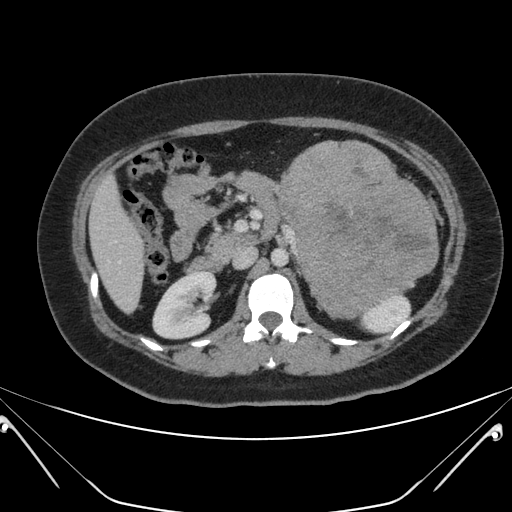
Contrast-enhanced abdominal CT, one axial slice. Slice 113 of 168 in the series (ordered by position). 120 kVp. Intravenous contrast given. Soft-tissue window (W 400 / L 40 HU). 3 mm slice thickness. 512 × 512 image matrix, field of view 394 × 394 mm. Patient: female, 26 years. From the clinical record (not read from this slice): diagnosis: adrenocortical carcinoma; tumour side: left adrenal; tumour size at pathology: 28 cm; Ki-67 index: 20 %; stage (as recorded): 2.
Structures marked on this image (semi-automatic segmentation, software-assisted and operator-edited):
- mass: bounding box (x1, y1, x2, y2) in pixels: (276, 140, 438, 317)